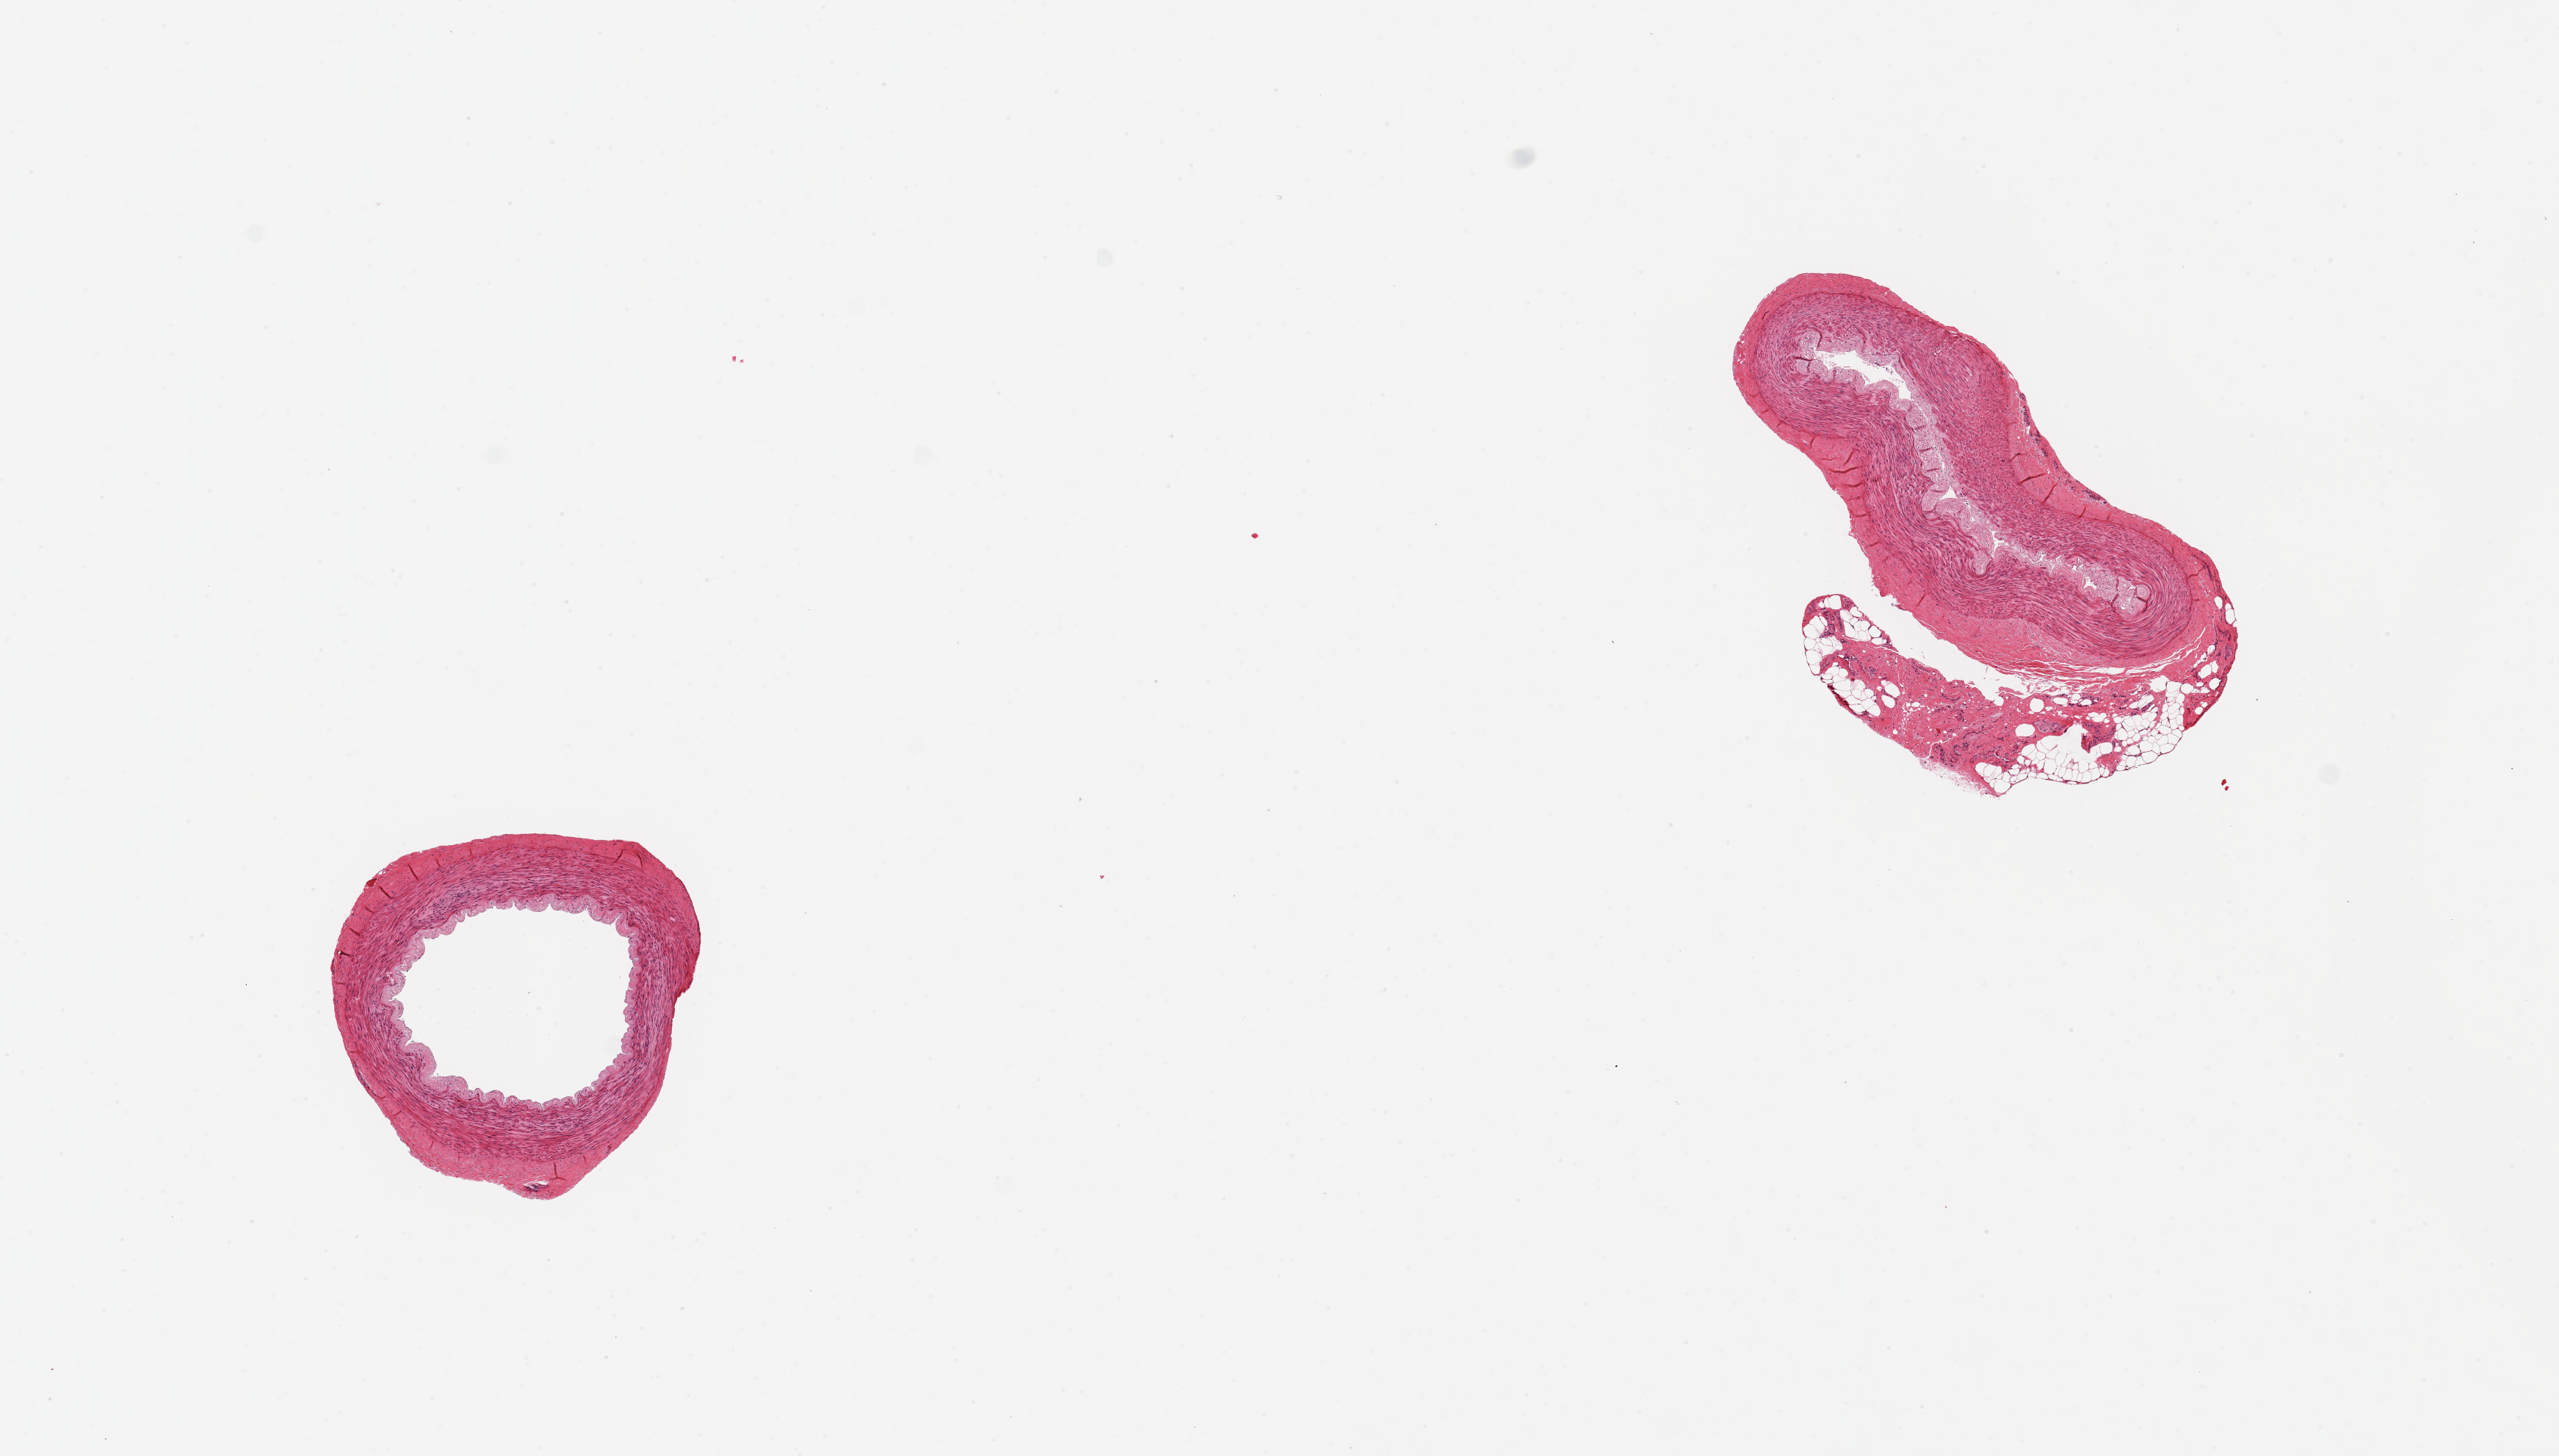
Whole-slide image, H&E stain — shown as a low-resolution overview of the whole scanned area (about 13.8 x 7.8 mm), PAXgene-fixed paraffin-embedded (PFPE) section, sampled site (target tissue): tibial artery, tissue donor sample. Male donor.
* review note (as recorded): 2 pieces; 1 has external fibrofatty tissue